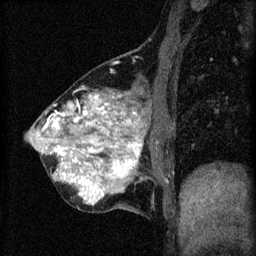
Breast MRI (dynamic contrast-enhanced), one sagittal slice. Slice 20 of 60 in the series (ordered by position). 3 images stored at this slice position (order not interpretable as contrast timing). 1.5 T. TE 4.2 ms, TR 8.2 ms. 2 mm slice thickness. 256 × 256 image matrix. Patient: female, 40 years.
Annotated regions visible in this slice (semi-automatically segmented with operator editing):
- analysis volume of interest (the breast-tissue region the enhancement analysis was run in; not a lesion): bounding box [x1, y1, x2, y2] px = [30, 78, 175, 213]
- tumour enhancement mask (voxels above the 70 % enhancement threshold inside the analysis volume of interest): [30, 96, 143, 205]